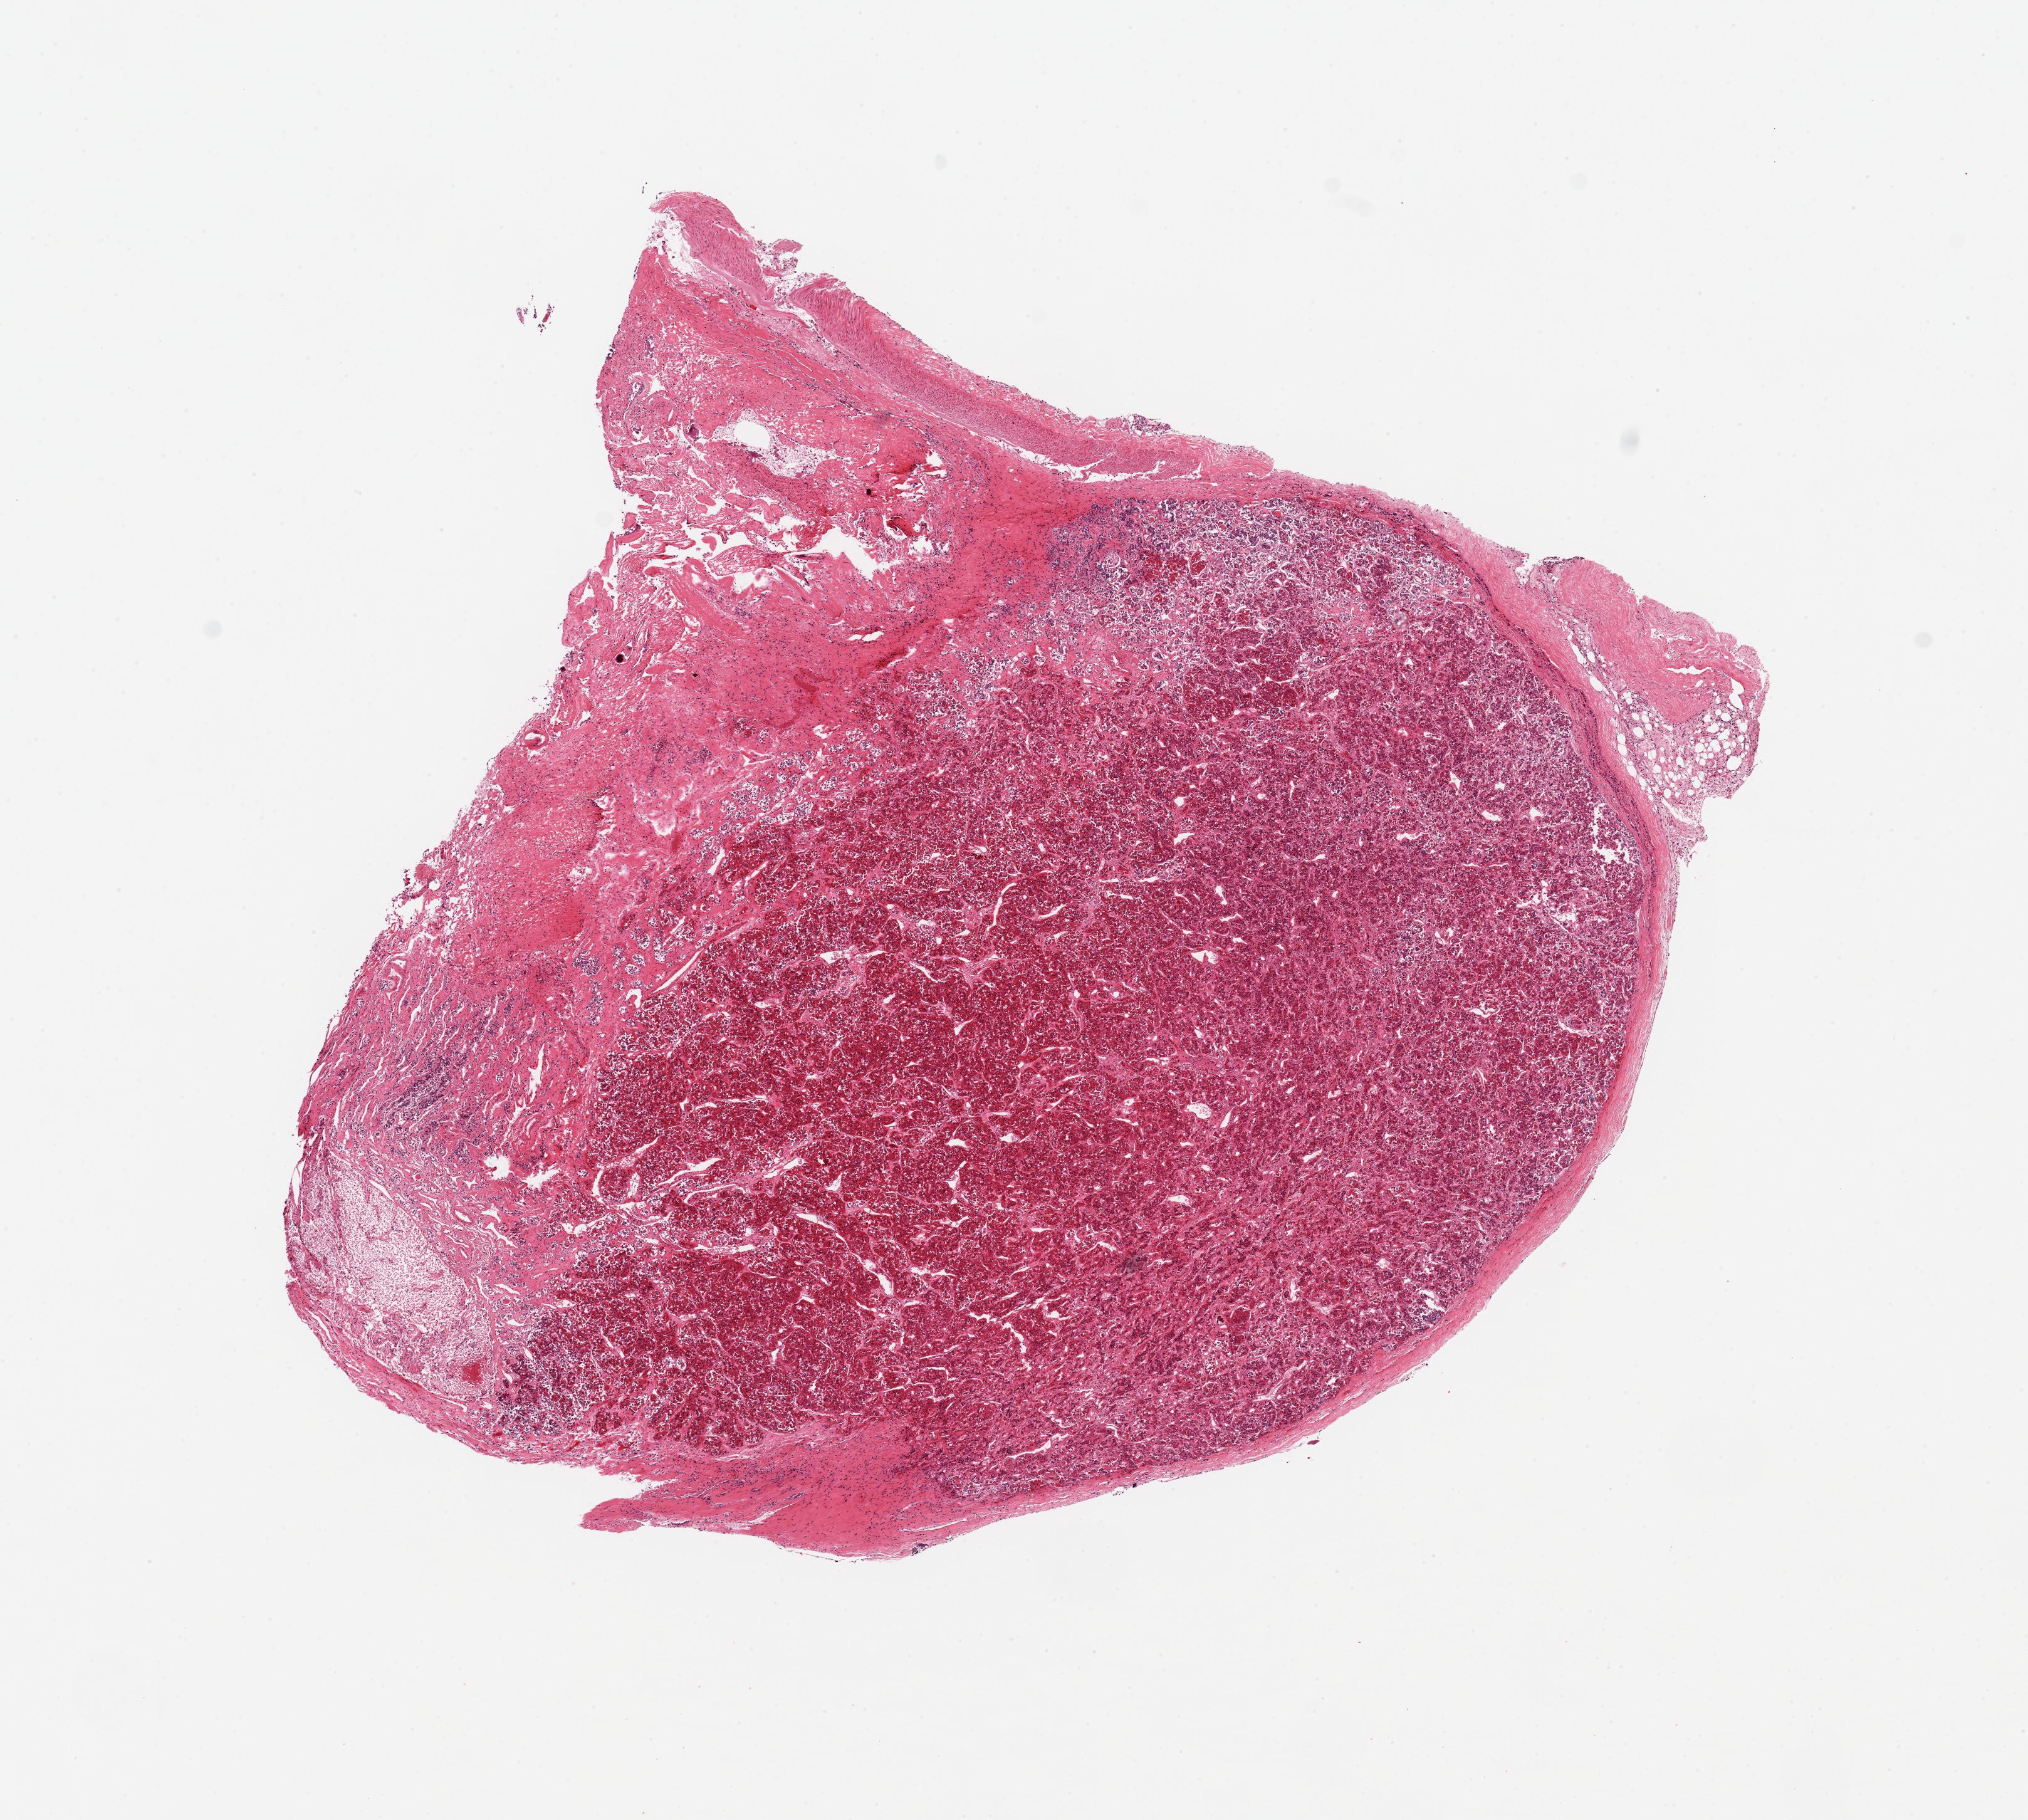
Haematoxylin and eosin whole-slide image, brightfield — low-resolution overview of the scanned area, about 12.8 x 11.5 mm. PAXgene-fixed paraffin-embedded (PFPE) section. Target tissue: pituitary. Donor tissue sample. Donor sex: male.
Pathologist's review note for this sample: 1 piece adenohypophysis, ~40% adherent dura.